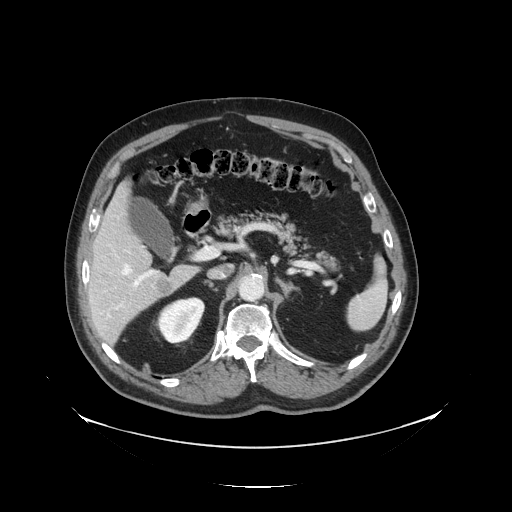
Contrast-enhanced abdominal CT, one axial slice. Position 79 of 138 along the scan axis. Reconstruction kernel STANDARD. 120 kVp. Intravenous contrast given. Soft-tissue window (W 400 / L 40 HU). 2.5 mm slice thickness. 512 × 512 image matrix. Male patient, age 77 years. Case-level facts recorded for this patient, not image findings: diagnosis: colorectal cancer liver metastases, imaged before liver resection; multiple liver metastases: no.
Structures marked on this image (manually delineated by an expert):
- hepatic veins: bounding box (x1, y1, x2, y2) in pixels: (122, 264, 132, 275)
- liver: (88, 185, 198, 344)
- planned liver remnant (the part of the liver to remain after resection): (88, 185, 154, 287)
- portal vein (with intrahepatic branches): (115, 253, 205, 310)
- liver metastasis: (157, 279, 174, 295)